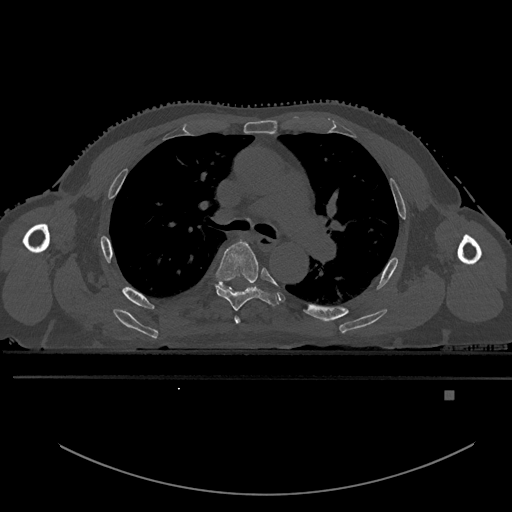
CT including the spine, one axial slice; slice 357 of 969 in the series (ordered by position); bone window (W 1800 / L 400 HU); 0.5 mm slice thickness; 512 × 512 image matrix, field of view 456 × 456 mm. Patient: male, 82 years. Case-level facts recorded for this patient, not image findings: primary cancer: prostate.
Outlined on this slice (semi-automatic segmentation, software-assisted and operator-edited):
- T4 vertebra: bounding box <234,316,241,324> (left, top, right, bottom; pixels)
- T5 vertebra: <215,240,278,311>